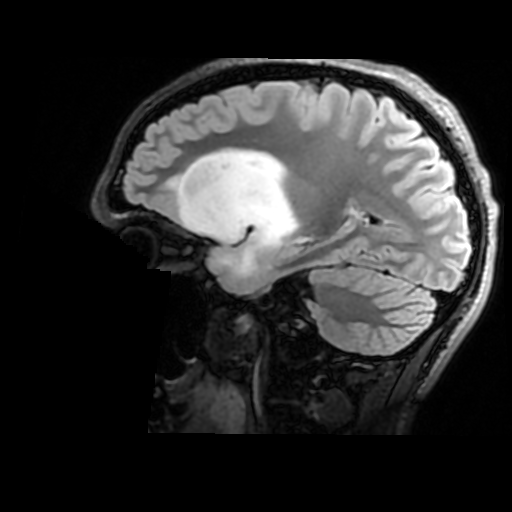
Brain MRI from a brain-tumour surgery series, one sagittal slice; position 112 of 176 along the scan axis; T2 FLAIR; 1 mm slice thickness; 512 × 512 image matrix. From the clinical record (not read from this slice): histopathology: Astrocytoma; WHO grade: 2; IDH mutation: yes; tumour location: Right Insular.
Outlined on this slice (expert manual segmentation):
- tumour: box from (x=178, y=149) to (x=296, y=283) px